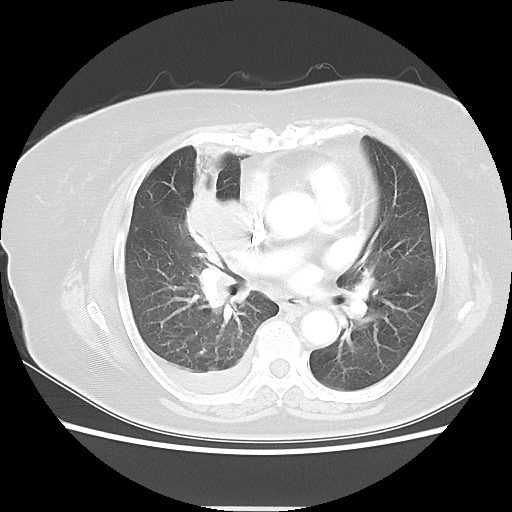
Chest CT, one axial slice; position 25 of 48 along the scan axis; reconstruction kernel LUNG; 120 kVp; lung window (W 1500 / L -600 HU); 5 mm slice thickness; 512 × 512 image matrix, field of view 360 × 360 mm. Female patient, age 73 years. From the clinical record (not read from this slice): clinical TNM (as recorded): T3 N3 M1b.
Annotated regions visible in this slice (bounding box drawn by a radiologist):
- lung tumour (recorded histology: small cell carcinoma): bounding box <171,178,263,311> (left, top, right, bottom; pixels)